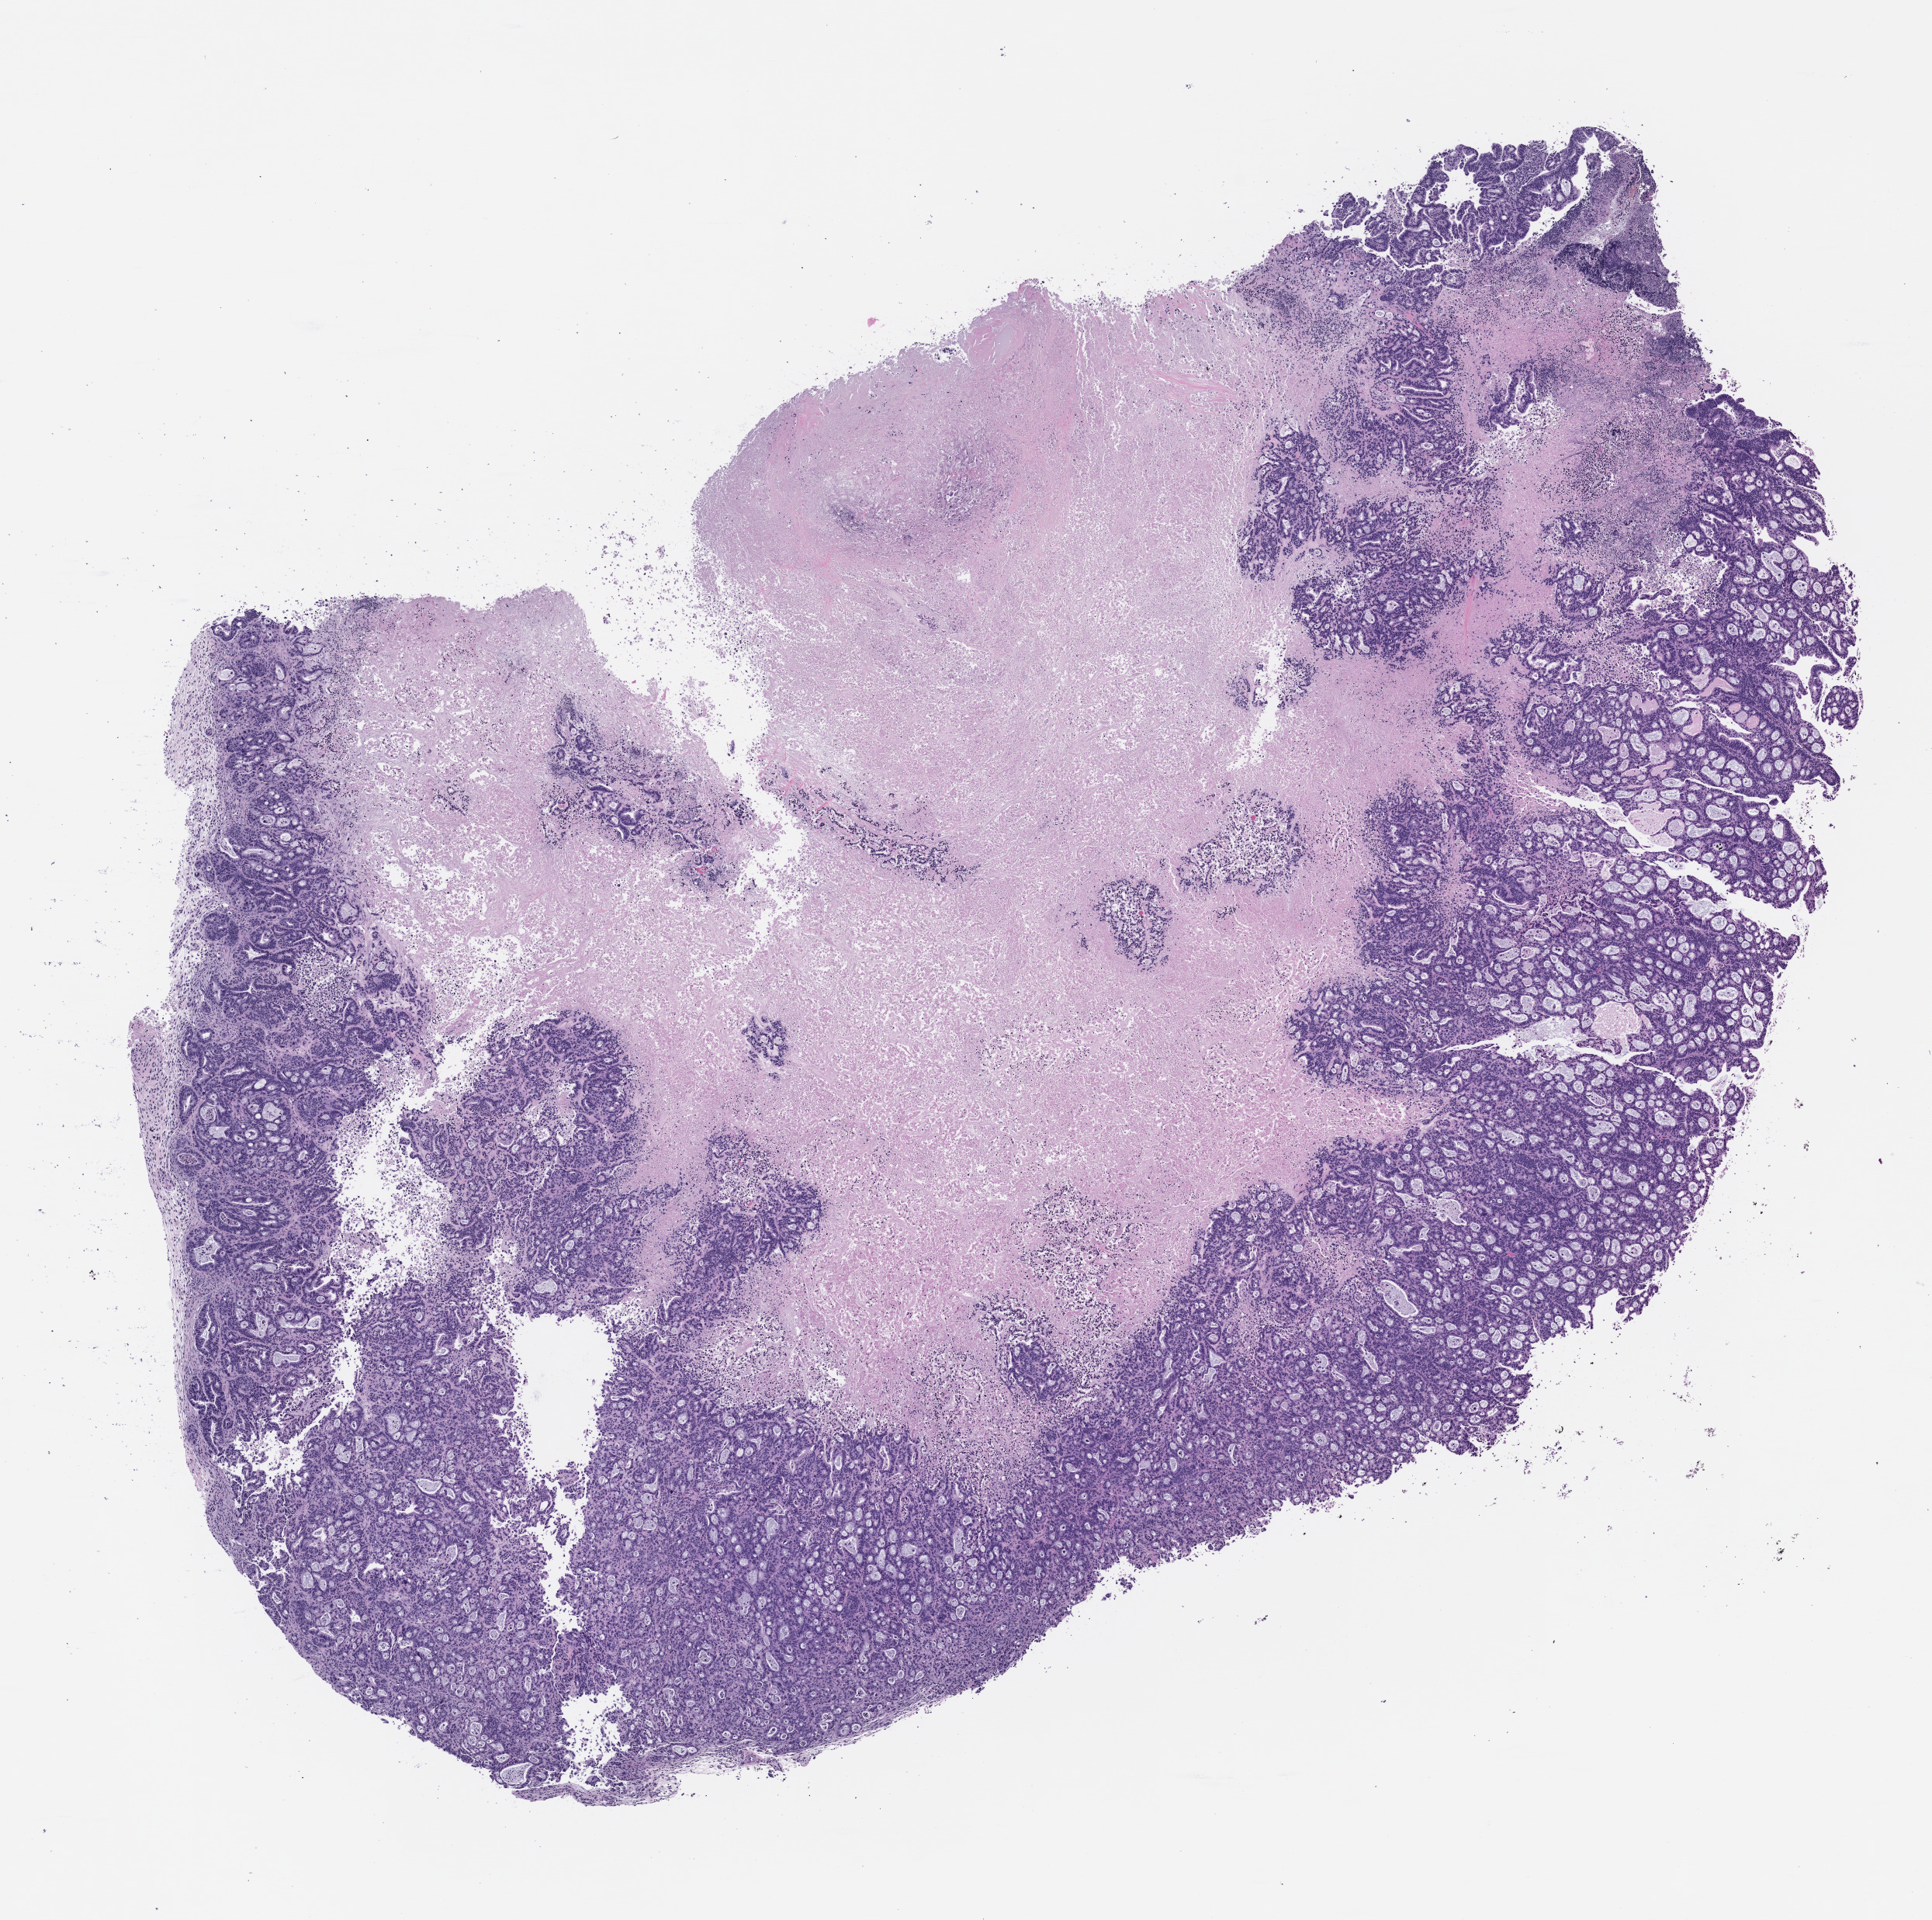
Whole-slide image, hematoxylin and eosin (H&E): patient-derived xenograft (human tumor grown in a mouse), passage 1 — low-resolution overview of the scanned area, about 10.0 x 9.9 mm; formalin-fixed, paraffin-embedded (FFPE) tissue; tumor site category: pancreas.
Originating patient diagnosis: Pancreatic Adenocarcinoma.